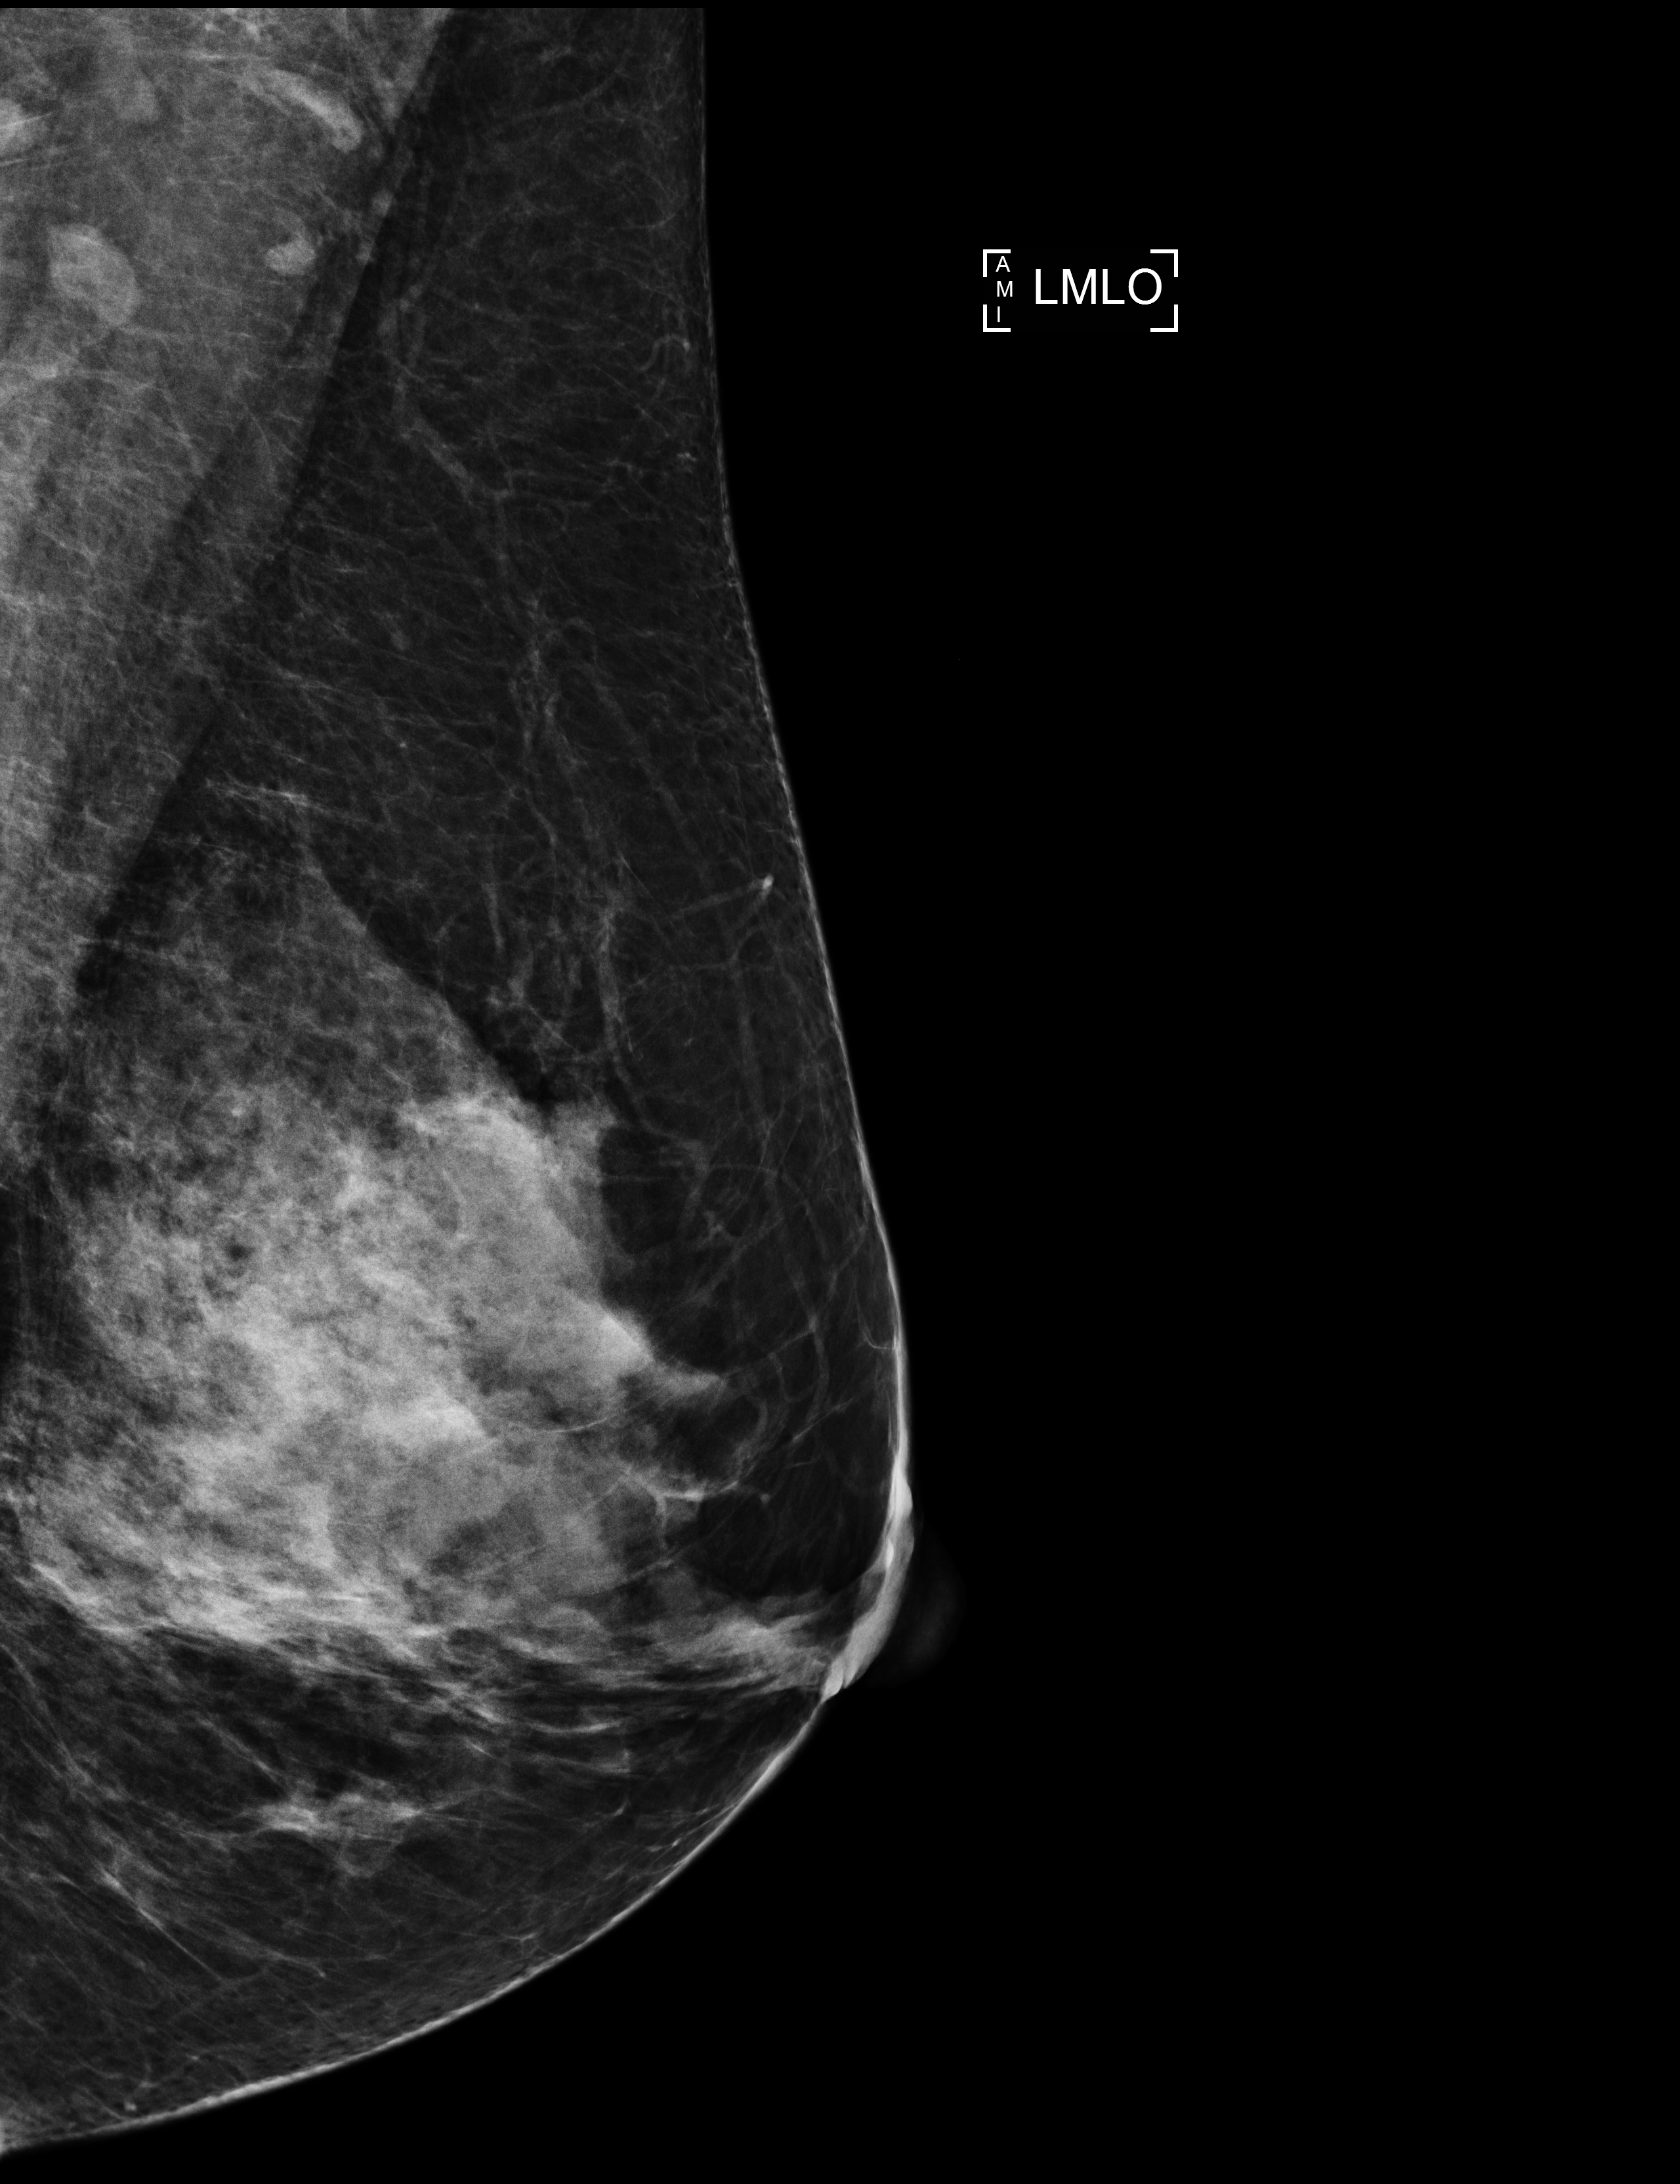
Screening examination; compressed breast thickness 68 mm.
Image type: full-field digital mammogram. Breast: left. Projection: mediolateral oblique (MLO) view.